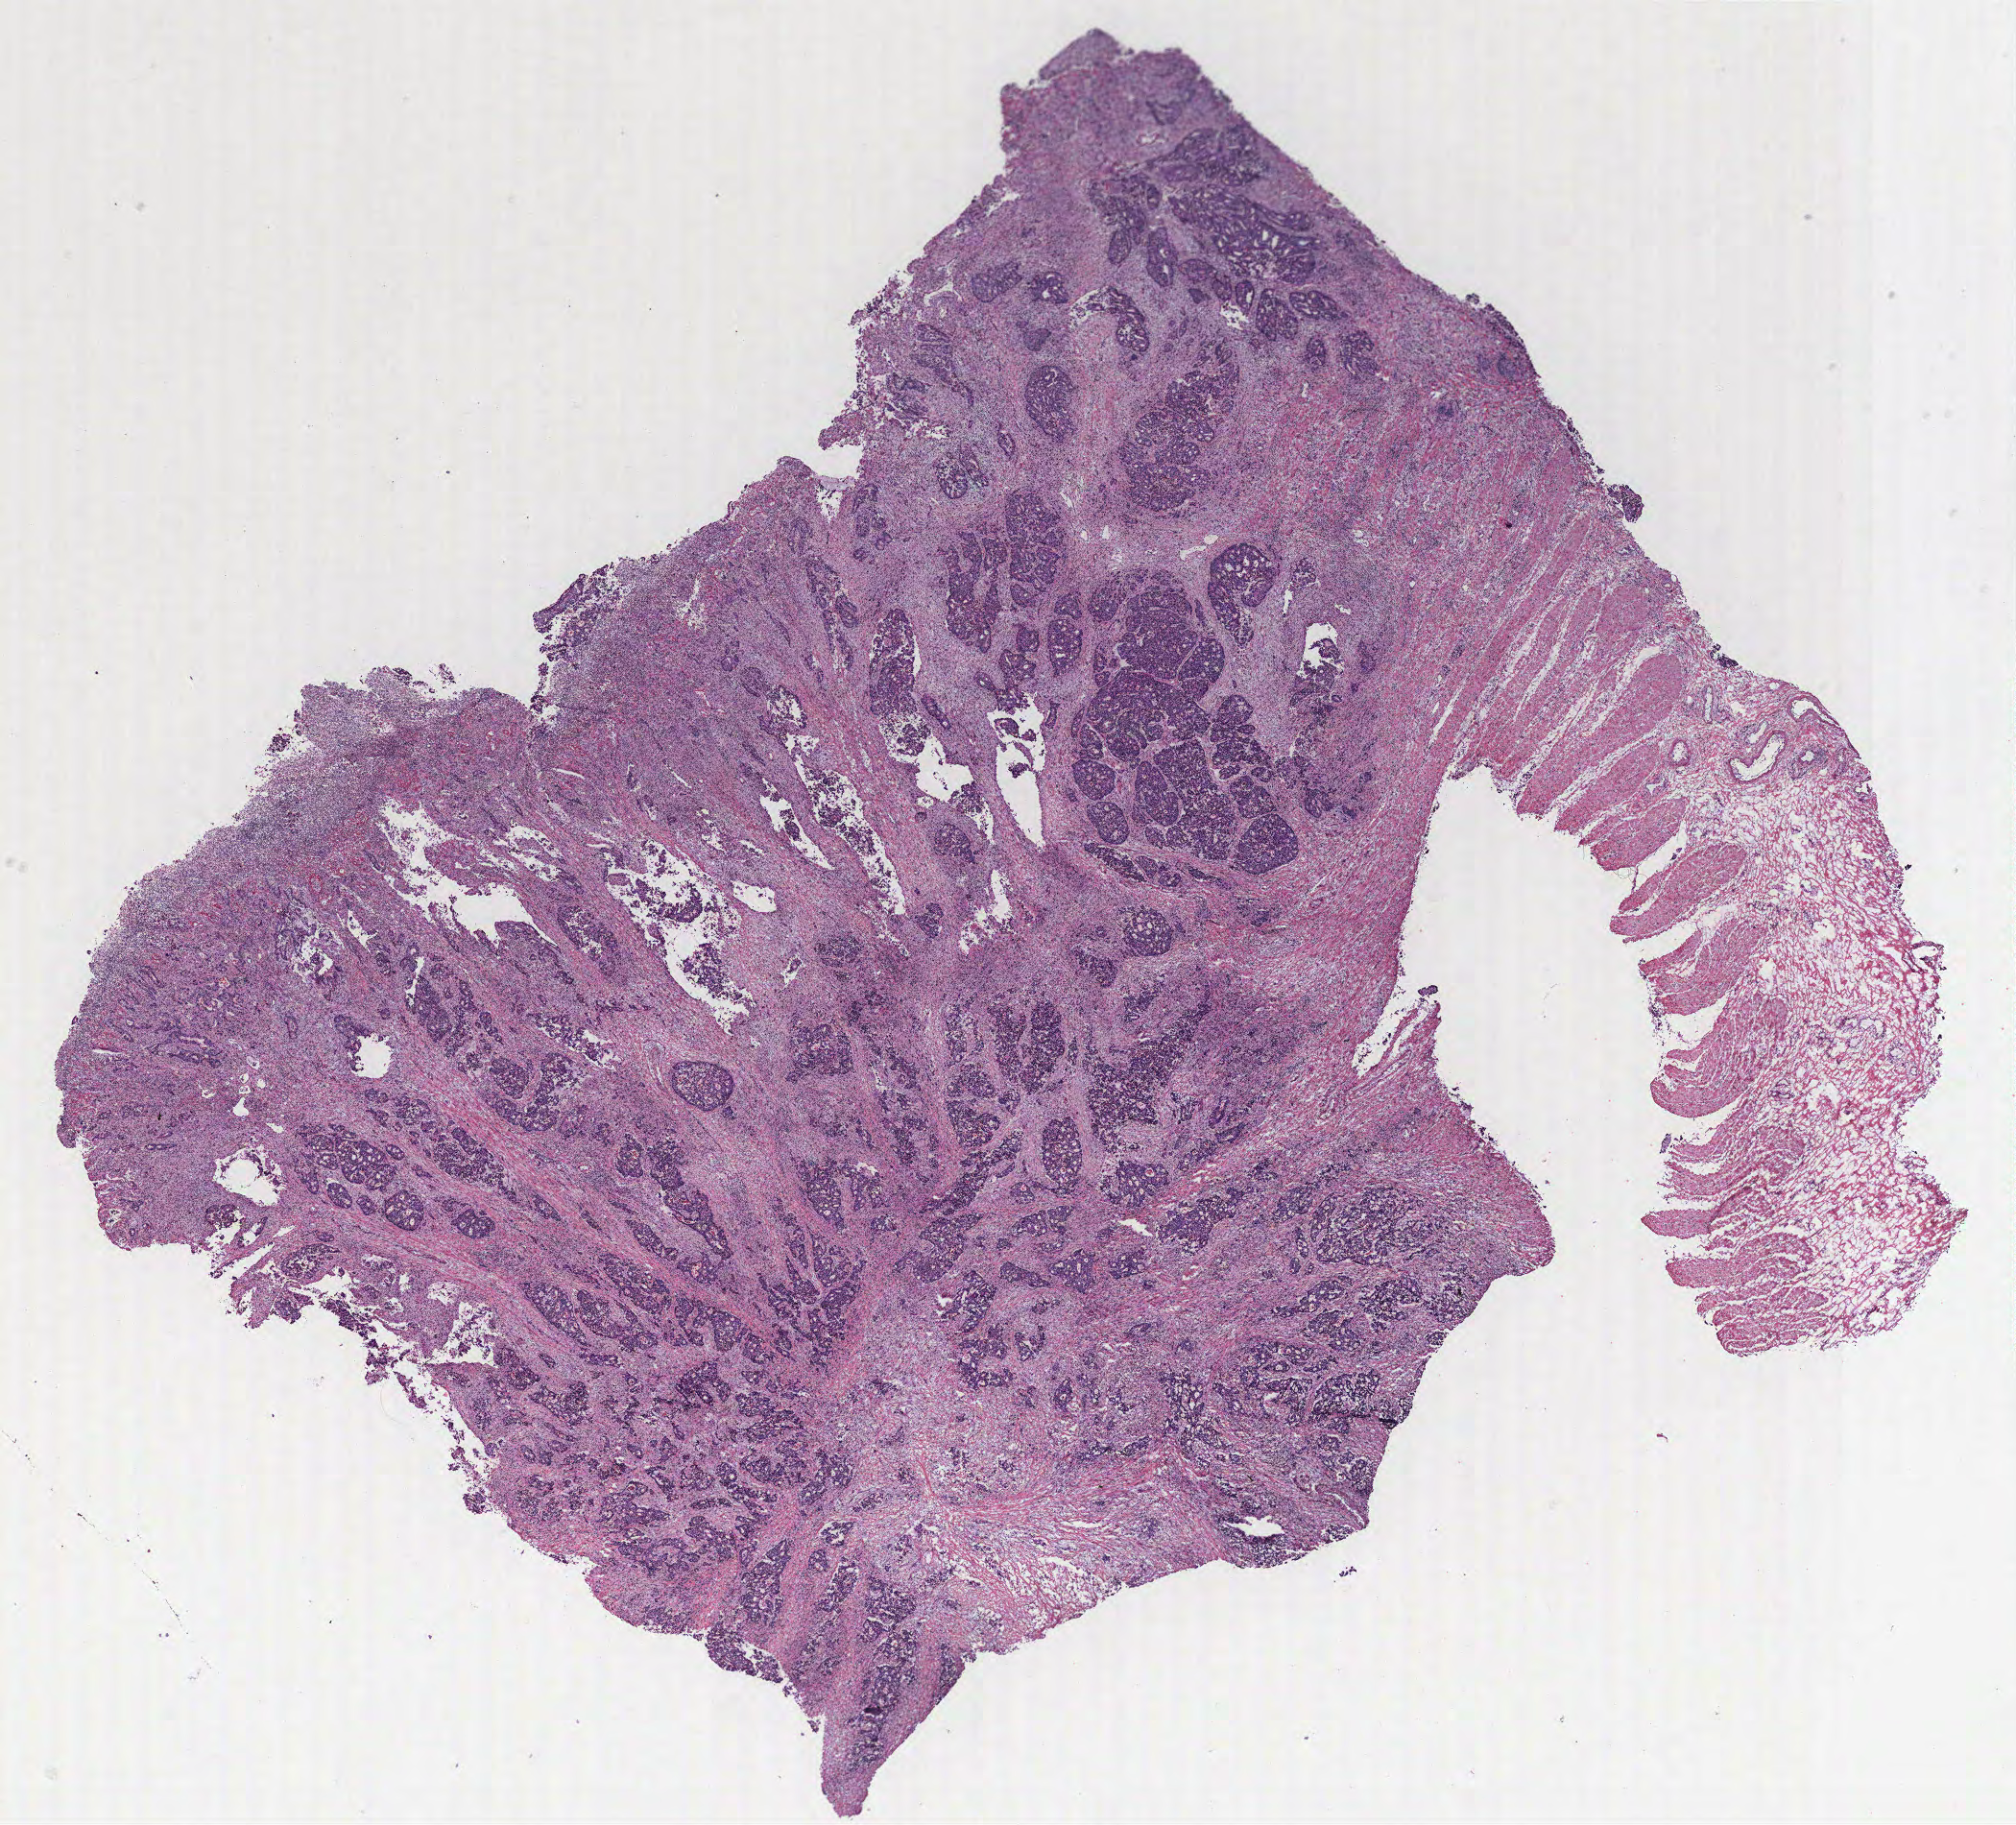
Whole-slide histology image, H&E — low-resolution overview of the scanned area, about 16.8 x 15.2 mm; colon, tissue type not recorded. Male patient.
Patient diagnosis: Adenocarcinoma, NOS.